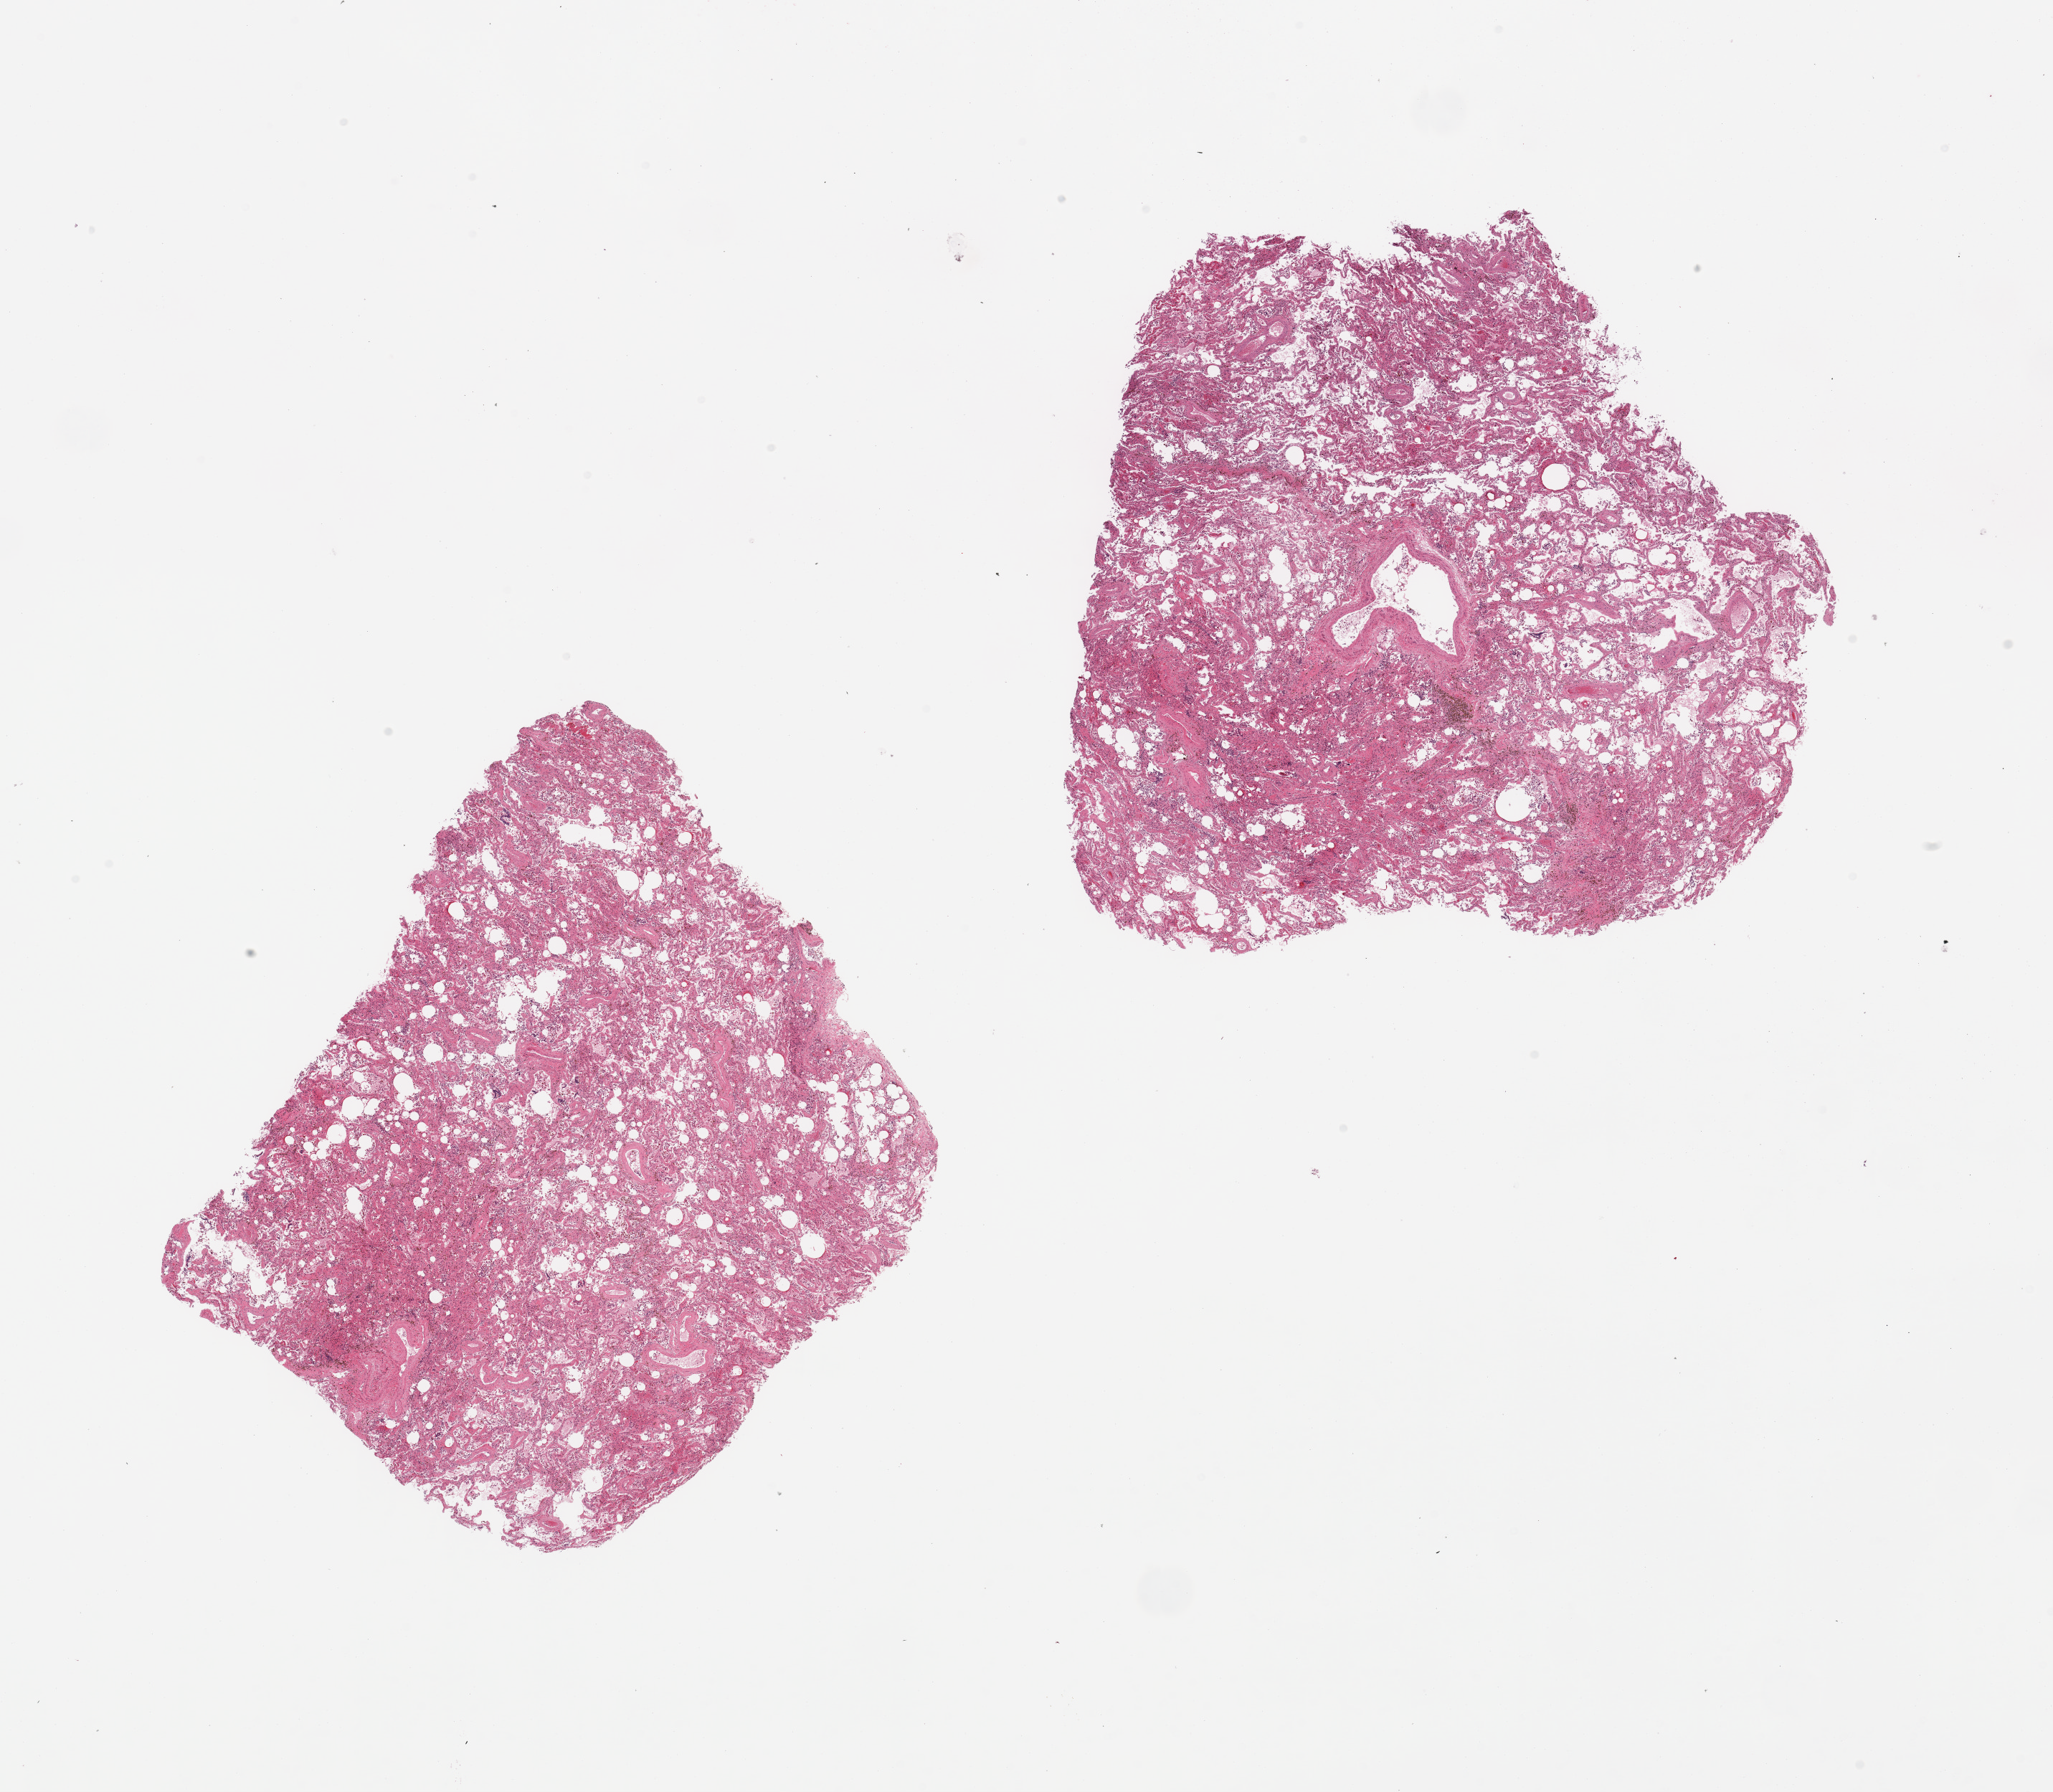
Digitized H&E-stained section, whole scanned area (about 22.6 x 19.8 mm, acquisition: 20x scan) shown as a low-resolution overview. PAXgene-fixed paraffin-embedded (PFPE) section. Target tissue: lung. Donor tissue sample.
Review note (as recorded): 2 pieces, moderate congestion.